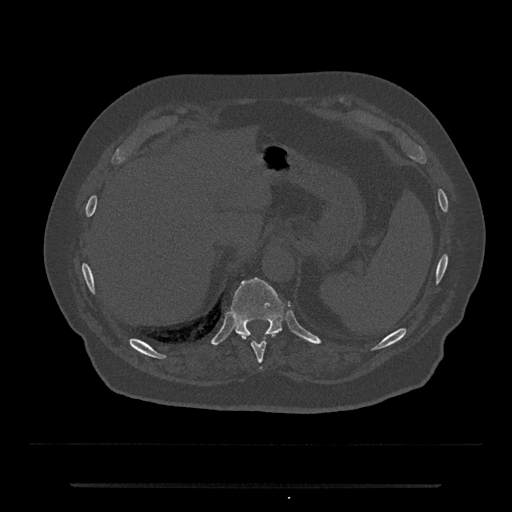
CT including the spine, one axial slice; slice 675 of 797 in the series (ordered by position); reconstruction kernel Br40s/3; 120 kVp; bone window (W 1800 / L 400 HU); 512 × 512 image matrix, field of view 434 × 434 mm. Patient: male, 80 years. From the clinical record (not read from this slice): primary cancer: prostate; vertebrae with lytic lesions (as recorded): L1, T11.
Annotated regions visible in this slice (semi-automatic segmentation, software-assisted and operator-edited):
- T10 vertebra: bounding box [x1, y1, x2, y2] px = [251, 333, 276, 370]
- T11 vertebra: [231, 277, 285, 337]